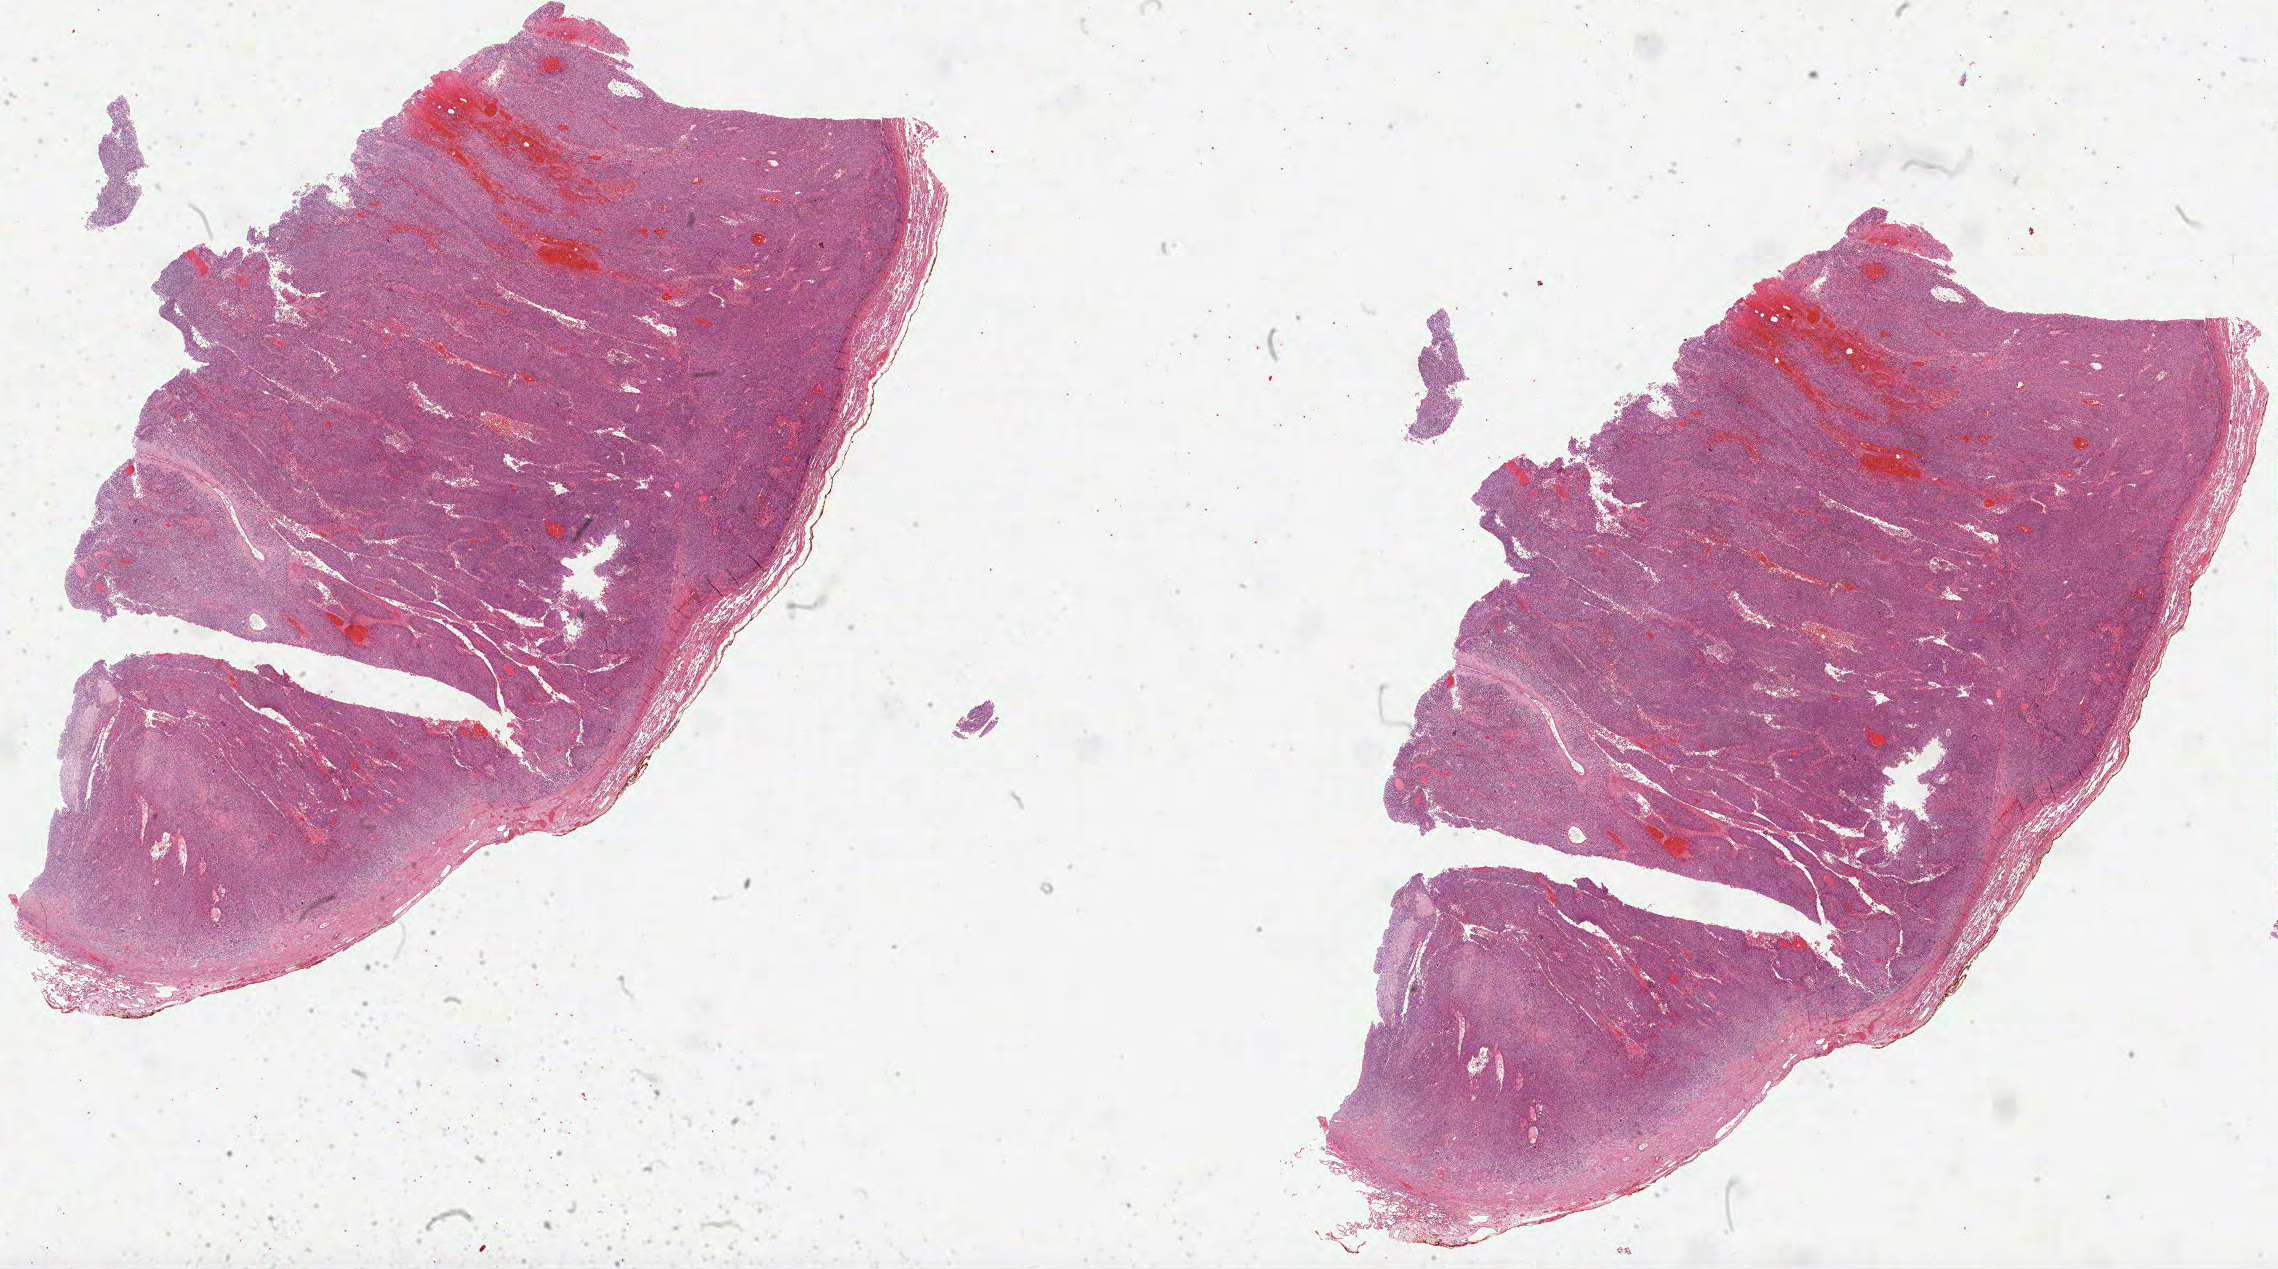
Digitized H&E-stained tissue section (whole slide), a low-resolution overview of the entire scanned area, about 36.7 x 20.5 mm, formalin-fixed paraffin-embedded (FFPE) diagnostic section, sample: primary tumour, lung. Patient: female, age at initial diagnosis 63 years.
Histologic diagnosis: Adenocarcinoma, NOS.